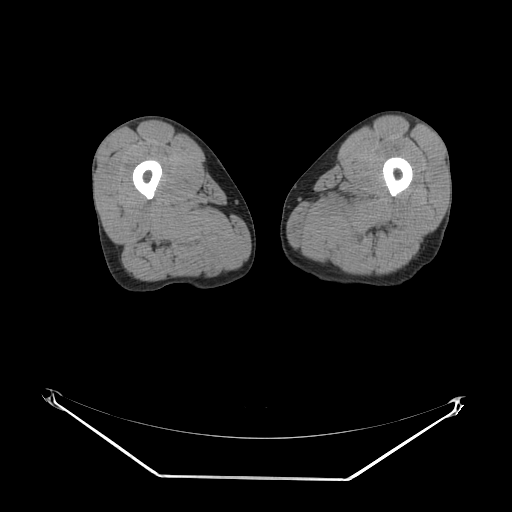
CT of an extremity soft-tissue mass (from a PET/CT study), one axial slice; slice 7 of 267 in the series (ordered by position); 140 kVp; soft-tissue window (W 400 / L 40 HU); 3.75 mm slice thickness; 512 × 512 image matrix. Male patient. From the clinical record (not read from this slice): histological type: pleiomorphic liposarcoma; grade: high; site of the primary tumour: left thigh.
Annotated regions visible in this slice (expert contour drawn on MRI and transferred to this co-registered scan by the dataset authors):
- gross tumour volume including surrounding oedema: bounding box <329,199,368,225> (left, top, right, bottom; pixels)